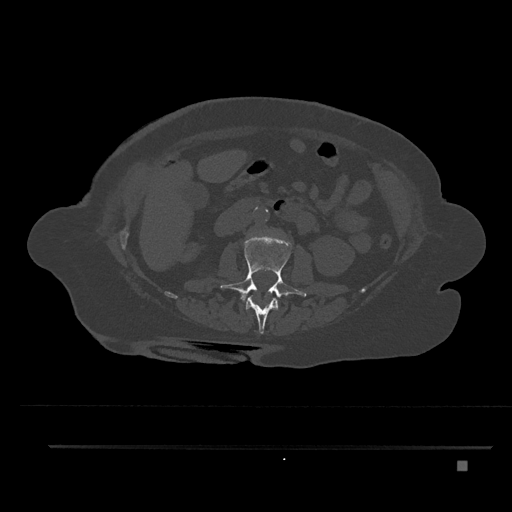
CT including the spine, one axial slice; position 179 of 797 along the scan axis; reconstruction kernel Br40s/3; 120 kVp; bone window (W 1800 / L 400 HU); 0.5 mm slice thickness; 512 × 512 image matrix, field of view 437 × 437 mm. Female patient, age 76 years. From the clinical record (not read from this slice): primary cancer: lung; vertebrae with lytic lesions (as recorded): T11, L3.
Annotated regions visible in this slice (semi-automatically segmented with operator editing):
- L1 vertebra: box from (x=245, y=296) to (x=279, y=334) px
- L2 vertebra: (x=220, y=236)–(x=307, y=302)